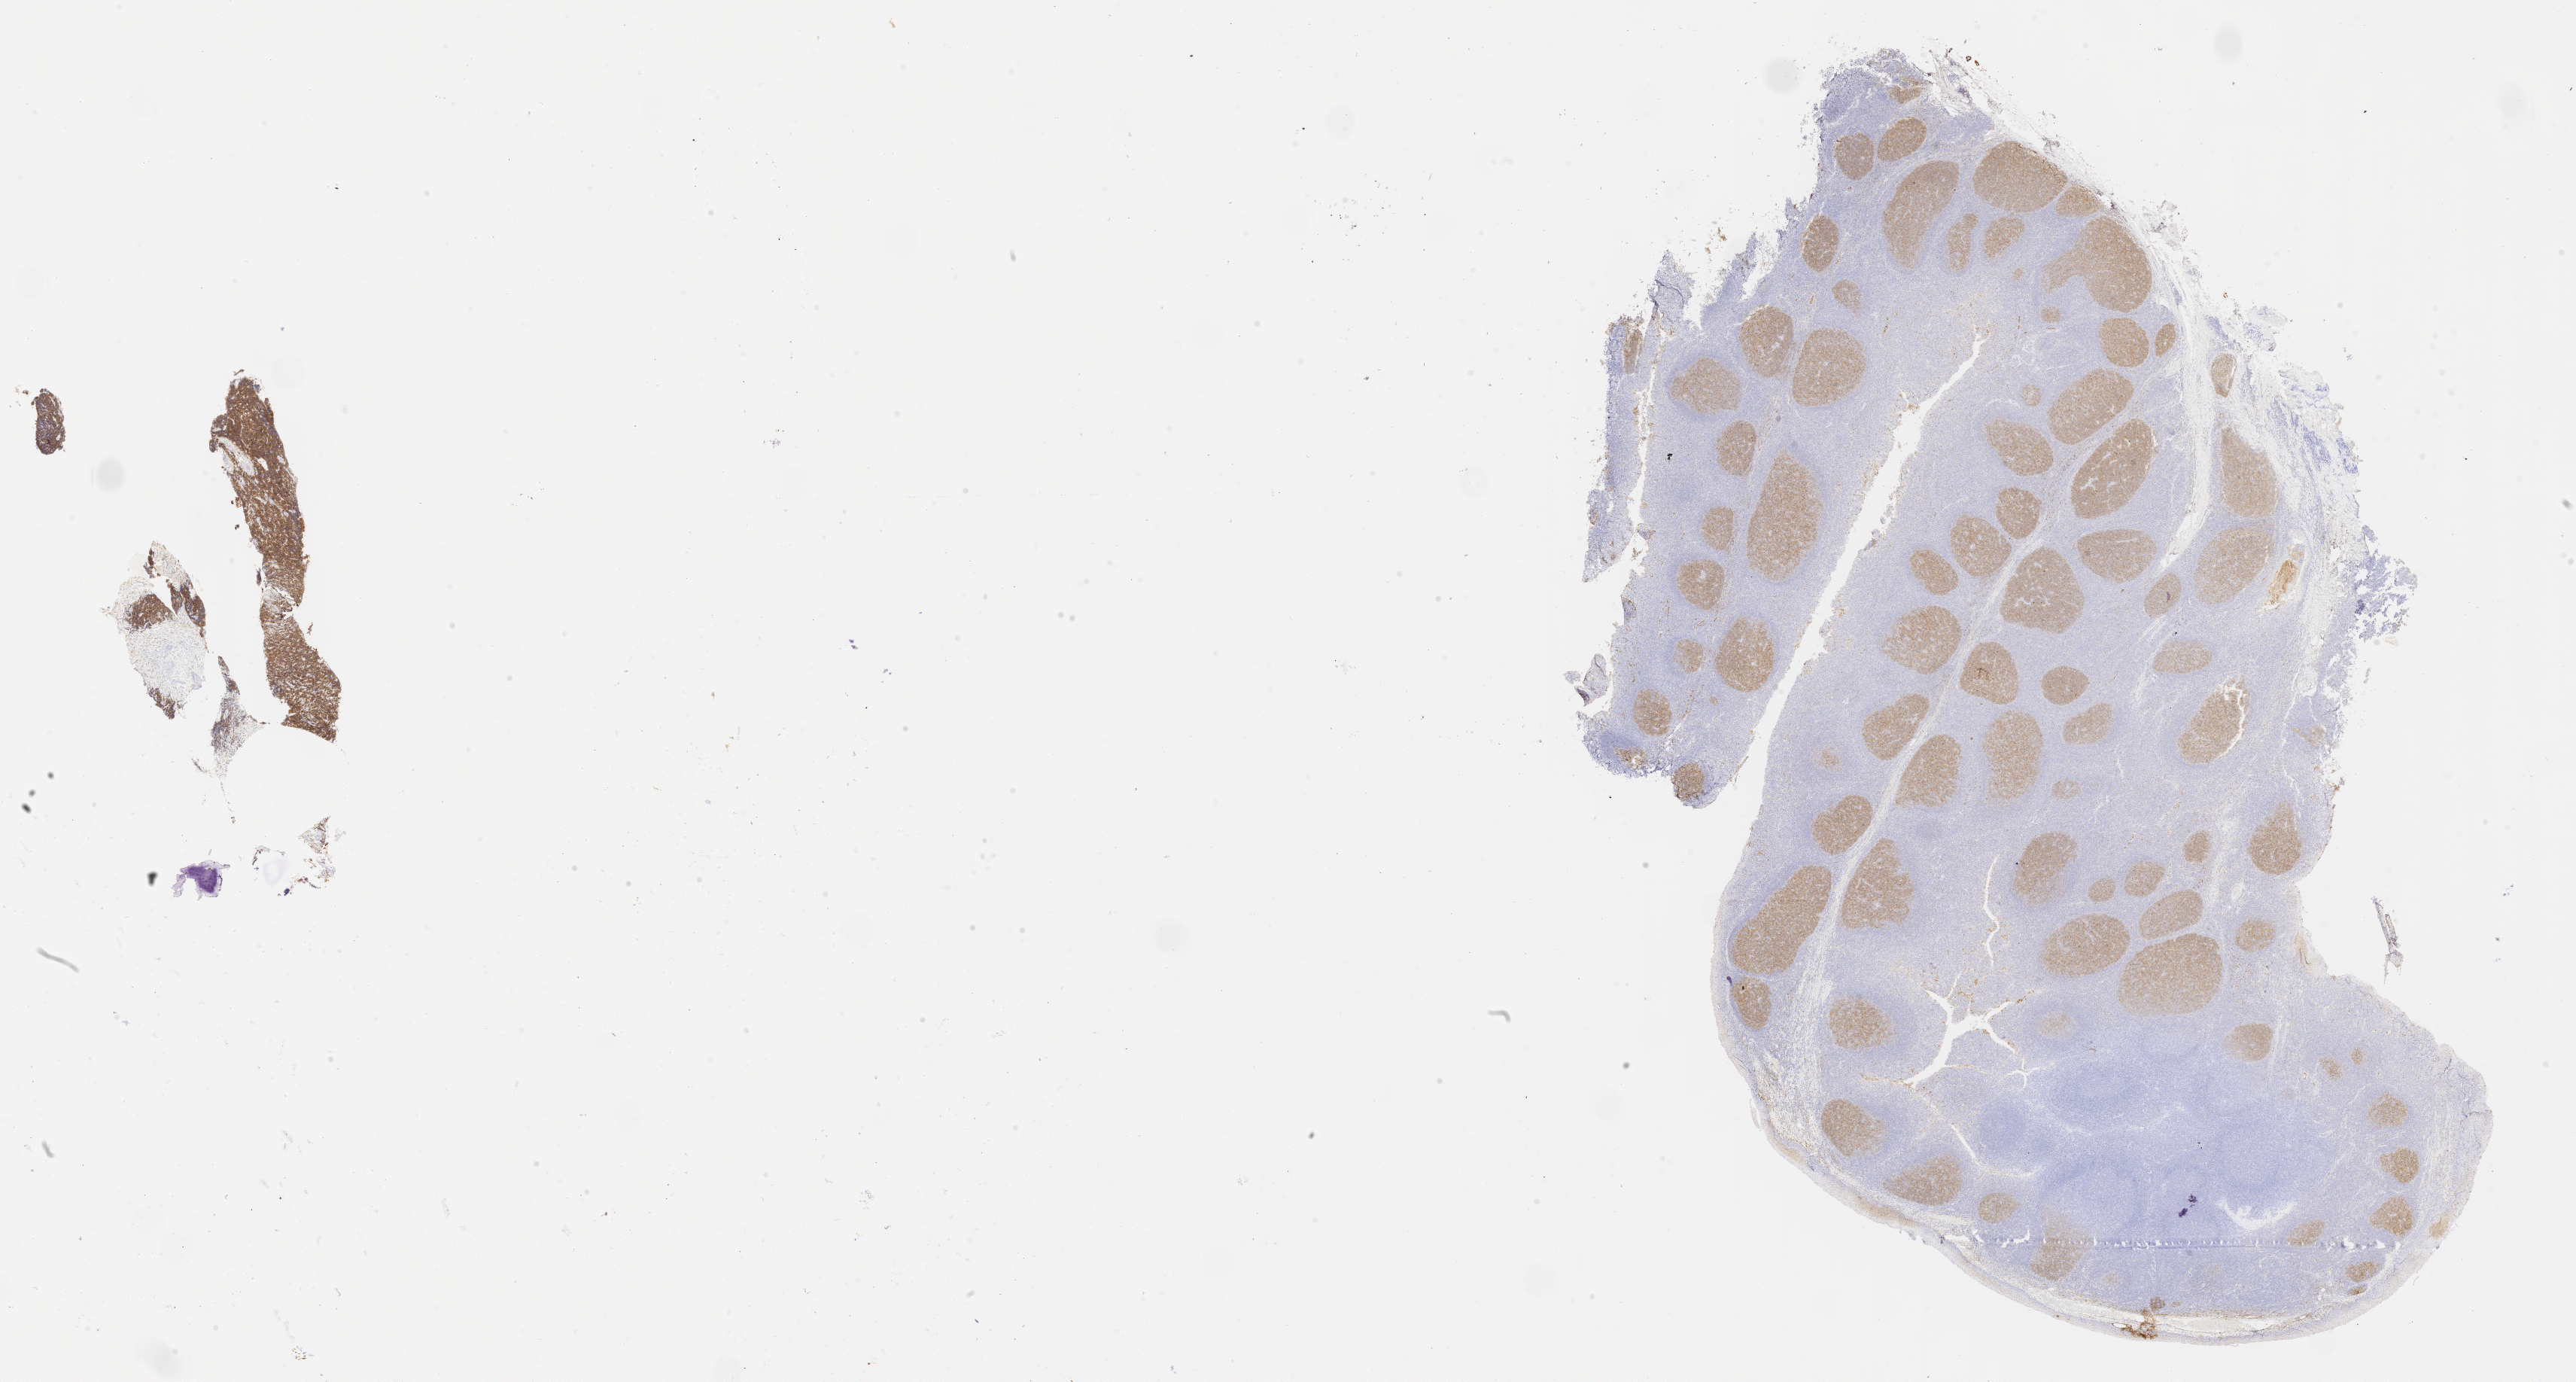
Immunohistochemistry (IHC) whole-slide image stained for CD10 — whole scanned area (about 27.7 x 14.8 mm) shown as a low-resolution overview; specimen: tumor tissue; site: mandible. Patient: male, age at initial diagnosis 6 years.
Diagnosis: Burkitt lymphoma, NOS.